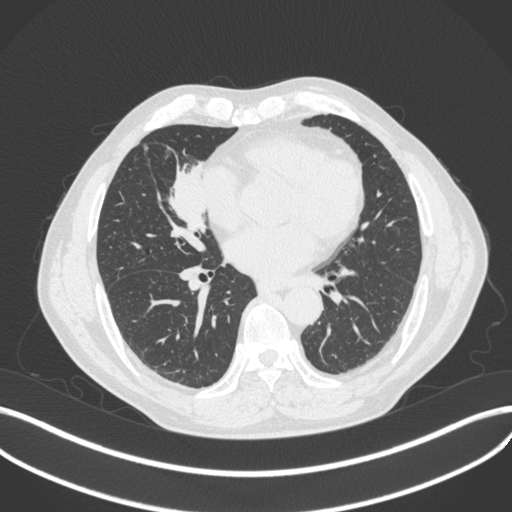
Chest CT, one axial slice; slice 177 of 429 in the series (ordered by position); reconstruction kernel B31f; lung window (W 1500 / L -600 HU); 1 mm slice thickness; 512 × 512 image matrix, field of view 400 × 400 mm. Male patient, age 61 years. Case-level facts recorded for this patient, not image findings: clinical TNM (as recorded): T2b N1 M0.
Outlined on this slice (bounding box drawn by a radiologist):
- lung tumour (recorded histology: squamous cell carcinoma): bounding box <162,150,216,243> (left, top, right, bottom; pixels)